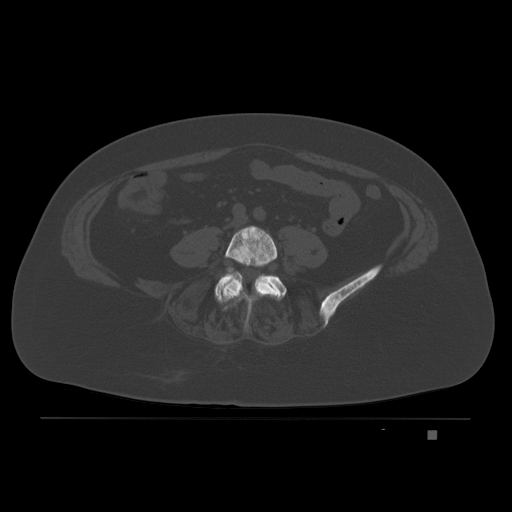
CT including the spine, one axial slice. Position 37 of 221 along the scan axis. Bone window (W 1800 / L 400 HU). 3 mm slice thickness. 512 × 512 image matrix, field of view 474 × 474 mm. Patient: female, 63 years. Case-level facts recorded for this patient, not image findings: primary cancer: breast.
Structures marked on this image (semi-automatically segmented with operator editing):
- L4 vertebra: bounding box <220,225,278,319> (left, top, right, bottom; pixels)
- L5 vertebra: <215,274,287,328>